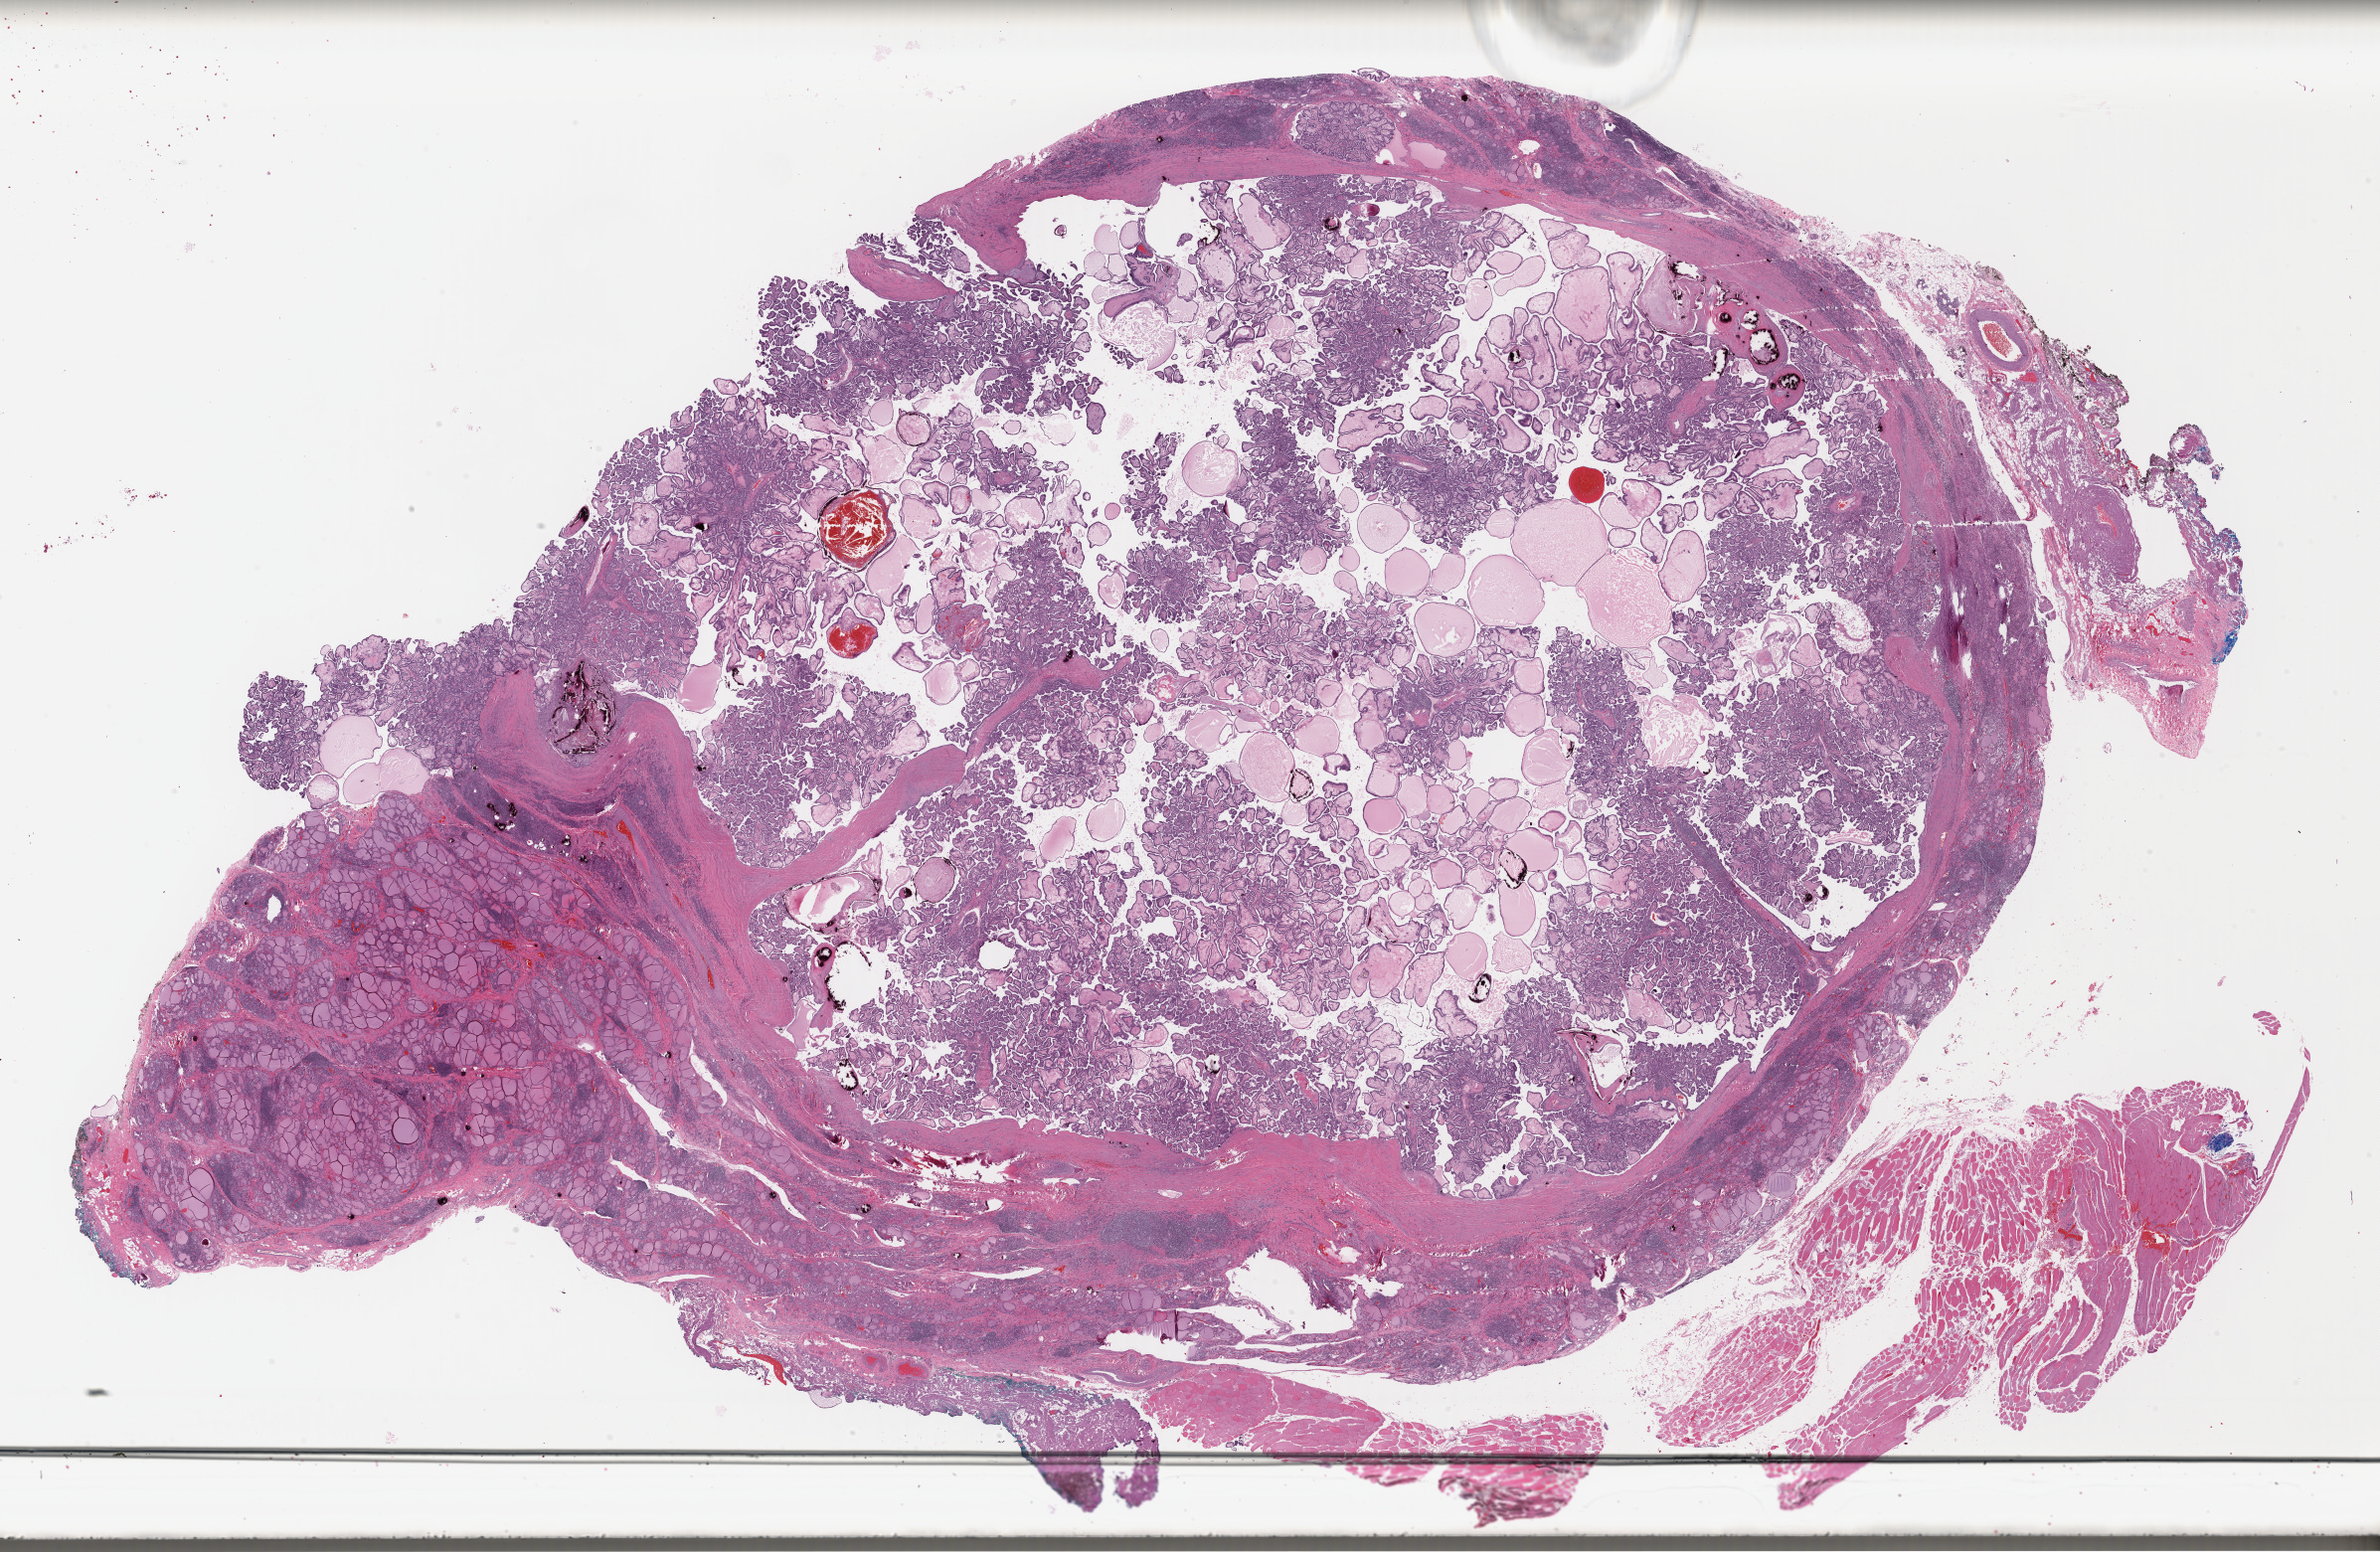
Whole-slide histology image, Hematoxylin and eosin (H&E) stained — shown as a low-resolution overview of the whole scanned area (about 37.6 x 24.5 mm, slide scanned at 40x); formalin-fixed paraffin-embedded (FFPE) diagnostic section; thyroid, primary tumour sample. Male patient; age at initial diagnosis 27 years.
AJCC pathologic stage: I (7th edition). Diagnosis: Papillary adenocarcinoma, NOS (thyroid gland). TNM: T3 N1a M0.